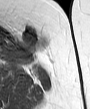
MRI of an extremity soft-tissue mass, one axial slice; position 26 of 45 along the scan axis; MR volume resampled by the dataset authors to the PET/CT grid (not the native acquisition matrix); 3.27 mm slice thickness; 90 × 109 image matrix. Female patient. Case-level facts recorded for this patient, not image findings: histological type: leiomyosarcoma; grade: intermediate; site of the primary tumour: parascapusular.
Annotated regions visible in this slice (expert contour drawn on MRI and transferred to this co-registered scan by the dataset authors):
- gross tumour volume including surrounding oedema: bounding box (x1, y1, x2, y2) in pixels: (19, 28, 47, 54)
- gross tumour volume (mass): (21, 28, 41, 47)